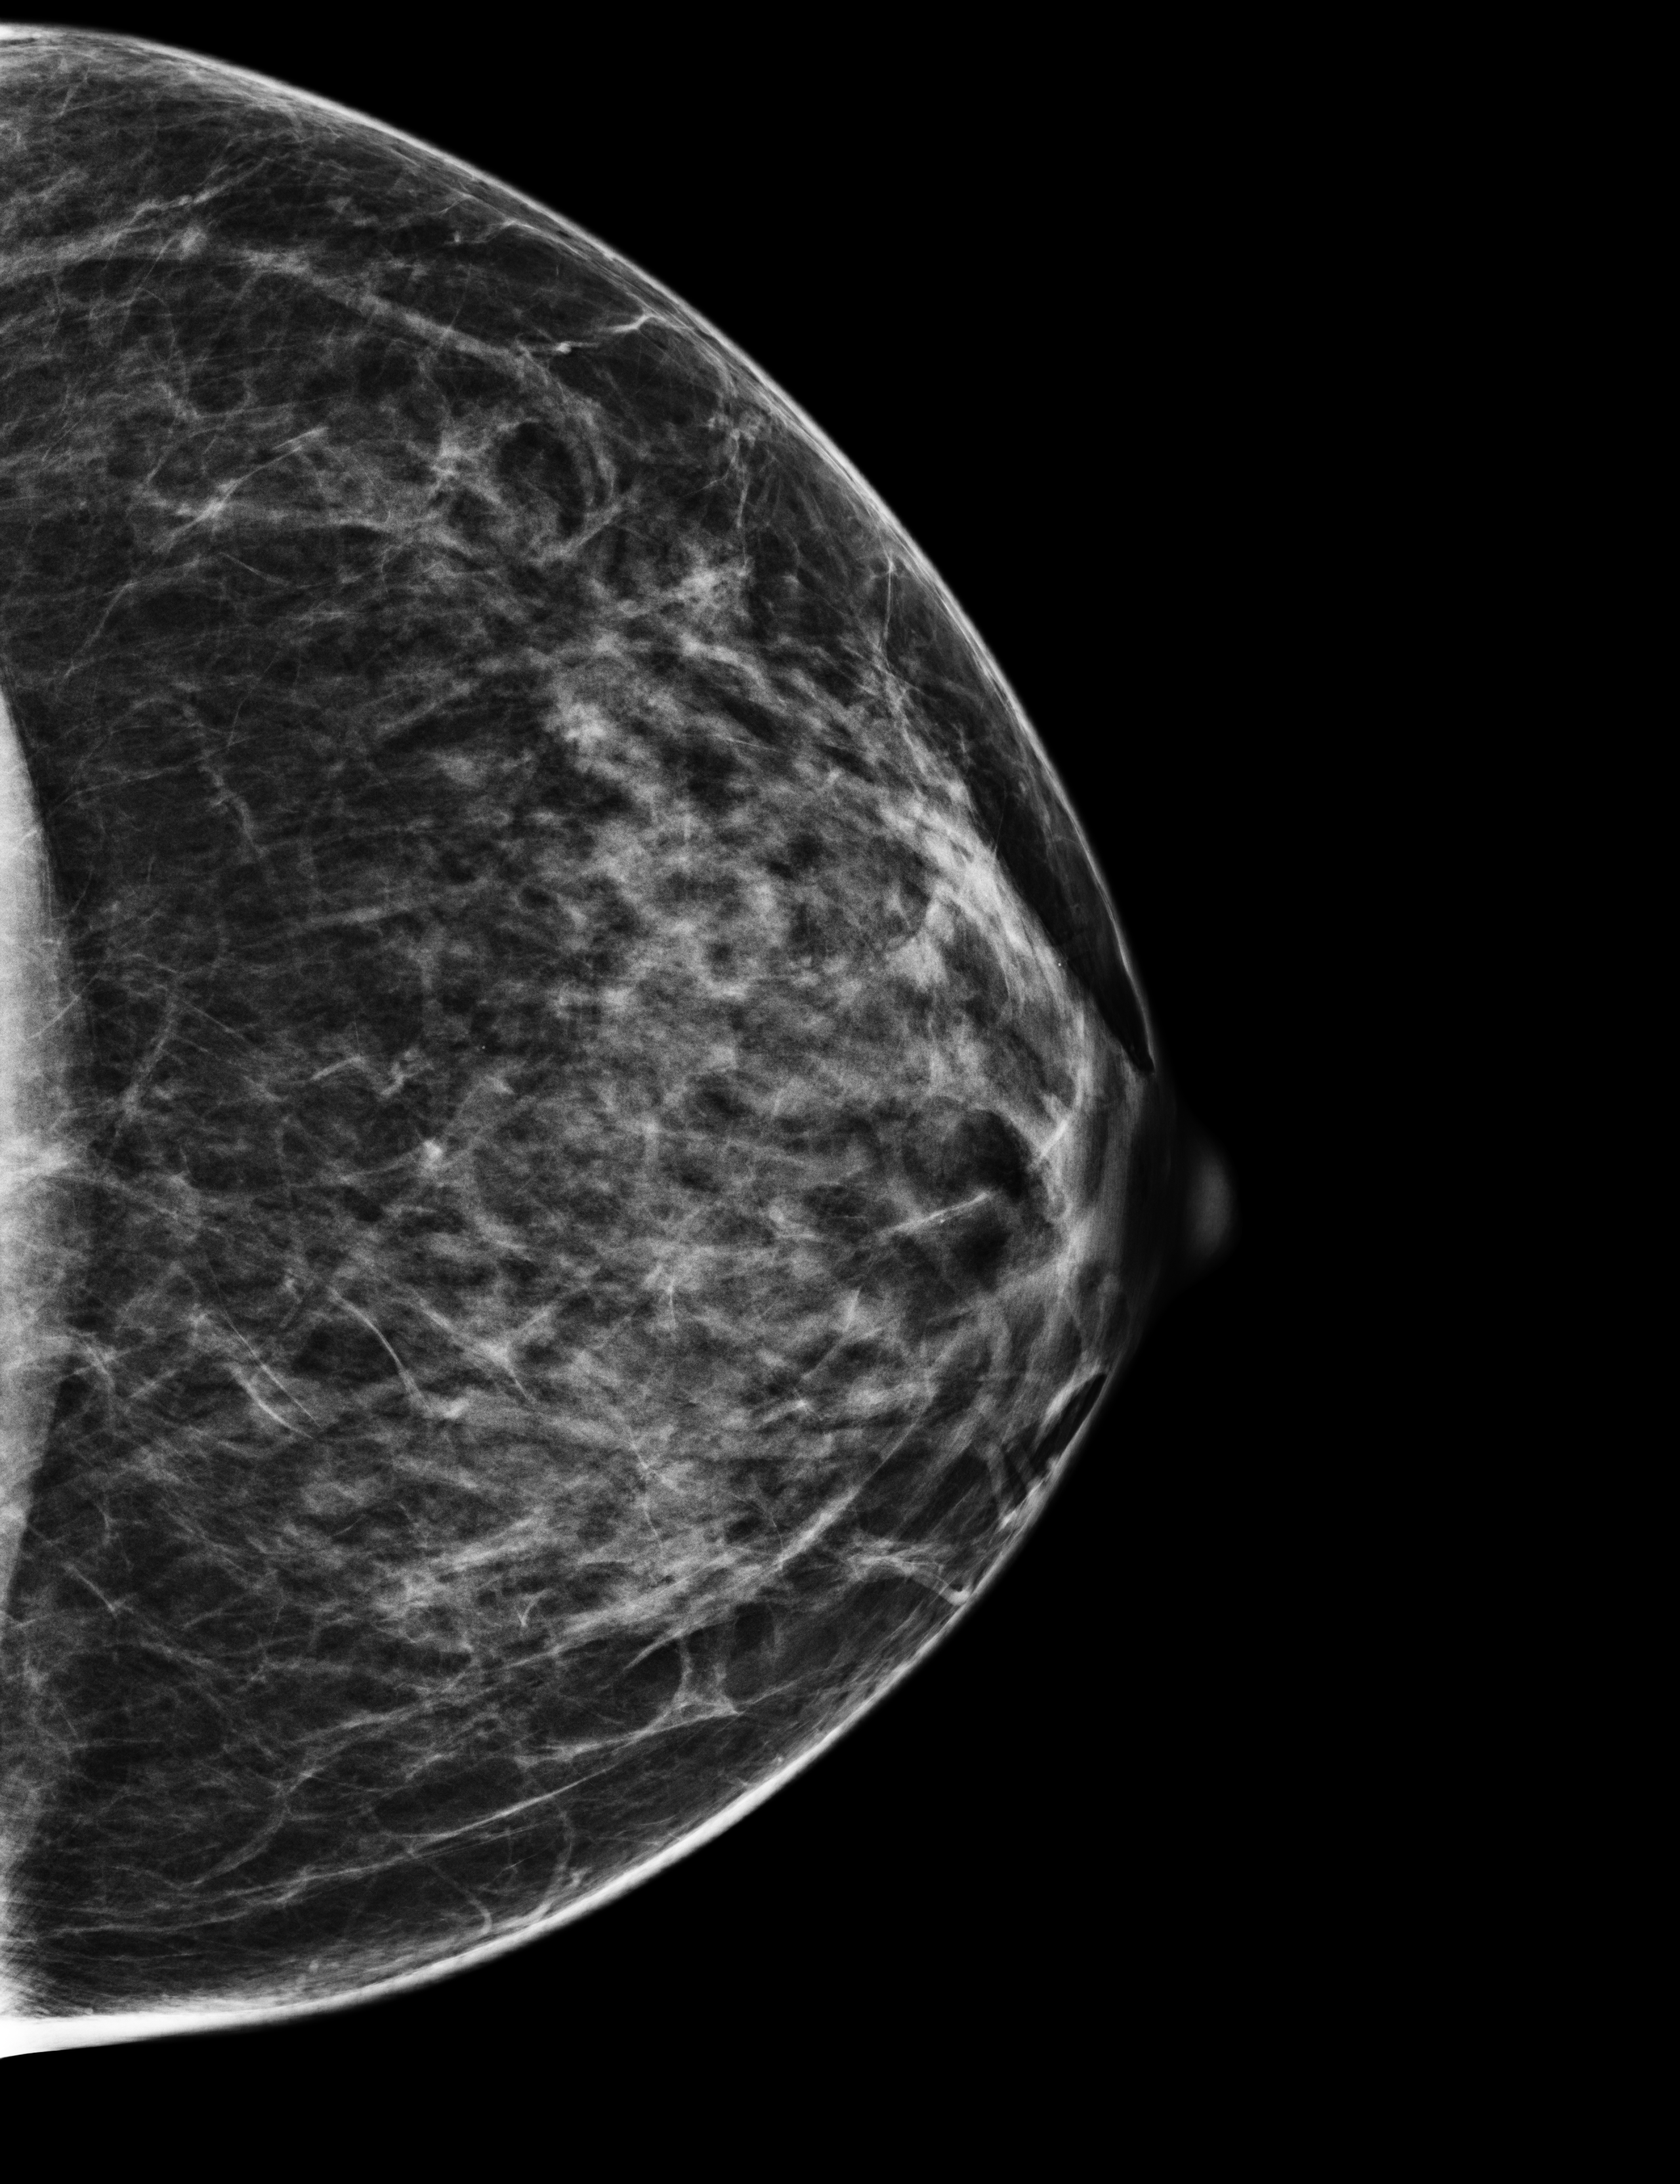
Digital mammogram (FFDM), left breast, CC view, annual screening mammography examination. Patient: female, 43 years.
- breast density at the screening exam (both breasts): heterogeneously dense (BI-RADS density category c)
- final BI-RADS category for the screening round (tomosynthesis exam, both breasts): category 1
- recall: no recall after this screen